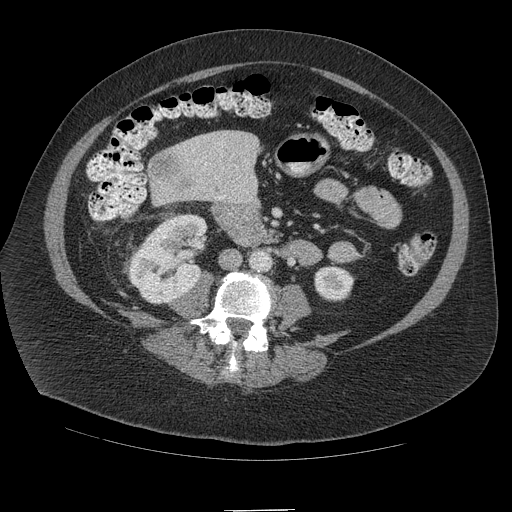
Contrast-enhanced abdominal CT (liver protocol), one axial slice; reconstruction kernel STANDARD; soft-tissue window (W 400 / L 40 HU); 2.5 mm slice thickness; 512 × 512 image matrix. From the clinical record (not read from this slice): diagnosis: hepatocellular carcinoma (patient treated with transarterial chemoembolisation; whether this scan precedes or follows treatment is not stated here); TNM stage (as recorded): Stage-IVB.
Structures marked on this image (semi-automatically segmented with operator editing):
- liver parenchyma outside the tumour (the mass and vessels are separate outlines, so this box may not span the whole liver): bounding box [x1, y1, x2, y2] px = [192, 130, 260, 180]
- mass: [147, 148, 192, 186]
- liver vessels: [203, 141, 224, 158]